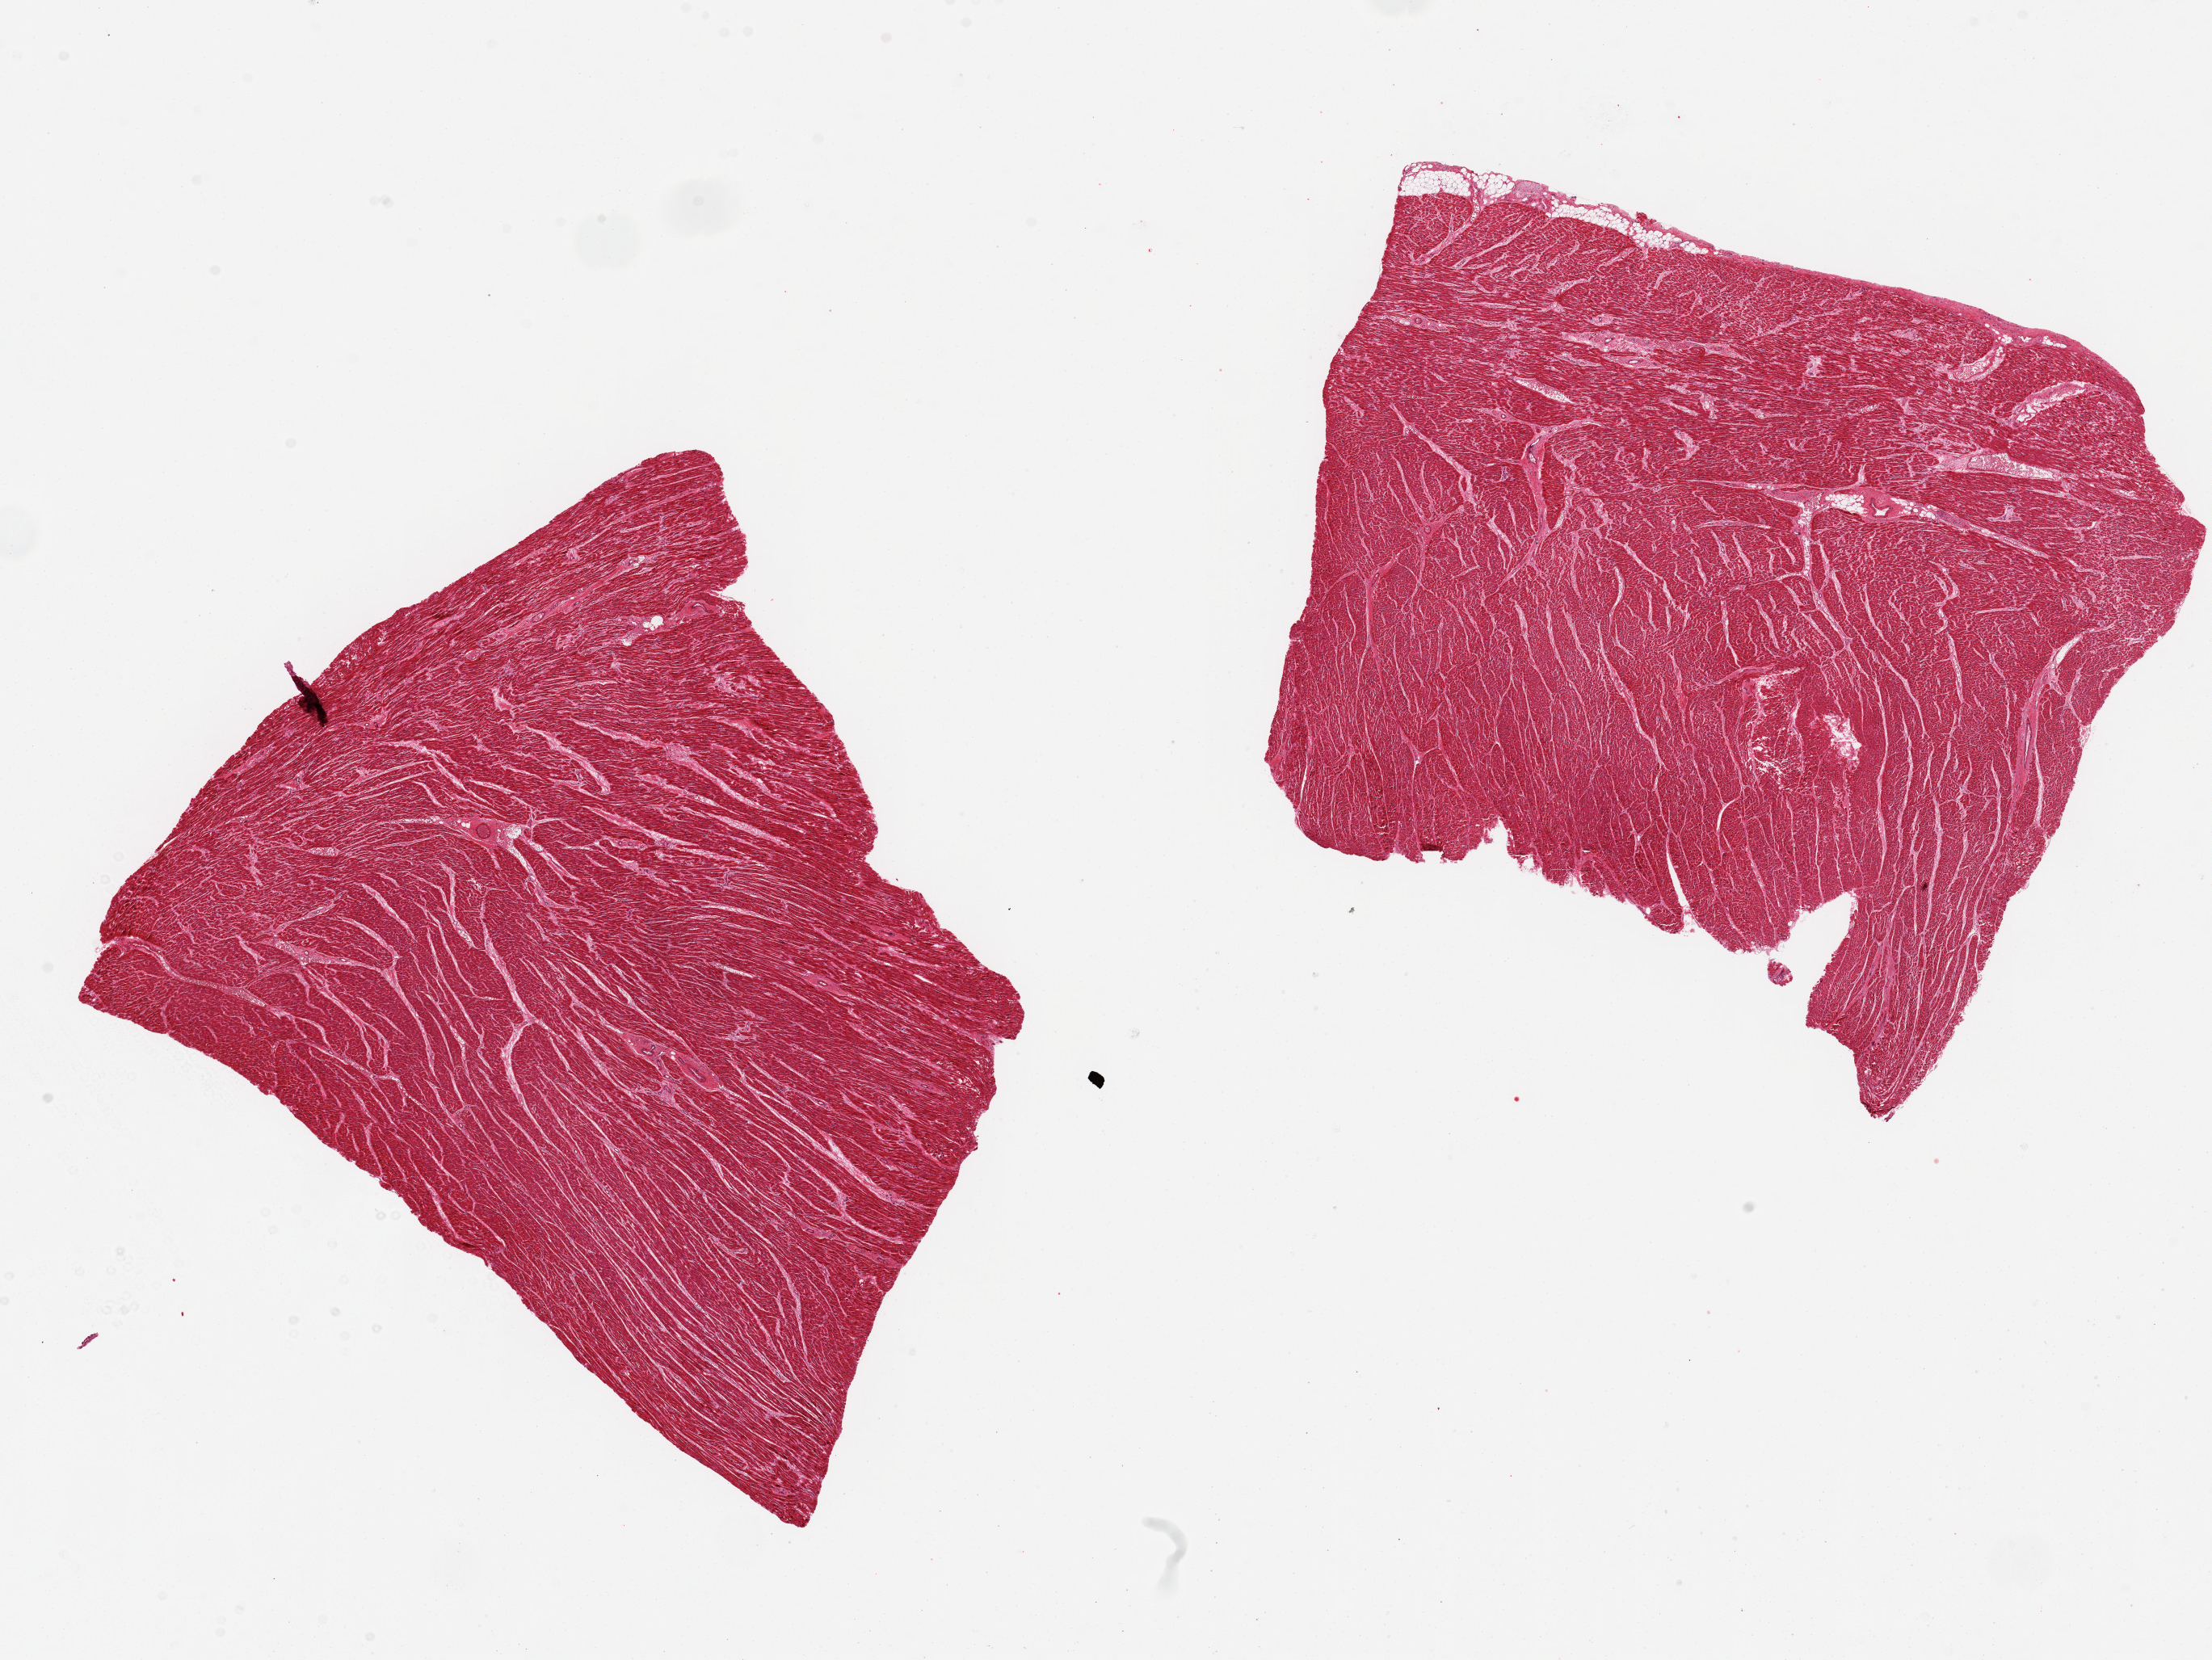
Whole-slide image, haematoxylin and eosin stain, shown as a low-resolution overview of the whole scanned area (about 21.7 x 16.3 mm). PAXgene-fixed paraffin-embedded (PFPE) section. Target tissue: heart. Tissue donor sample. Donor sex: male.
Review note (as recorded): 2 pieces, 7.4x8.7 & 7.7x6.5 mm.